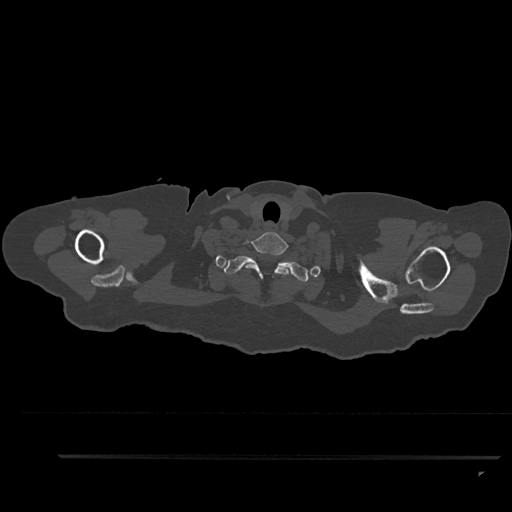
CT including the spine, one axial slice. Slice 779 of 797 in the series (ordered by position). Bone window (W 1800 / L 400 HU). 512 × 512 image matrix, field of view 408 × 408 mm. Patient: female, 44 years. From the clinical record (not read from this slice): primary cancer: renal; vertebrae with lytic lesions (as recorded): L1.
Structures marked on this image (semi-automatic segmentation, software-assisted and operator-edited):
- T1 vertebra: bounding box (x1, y1, x2, y2) in pixels: (224, 255, 309, 282)